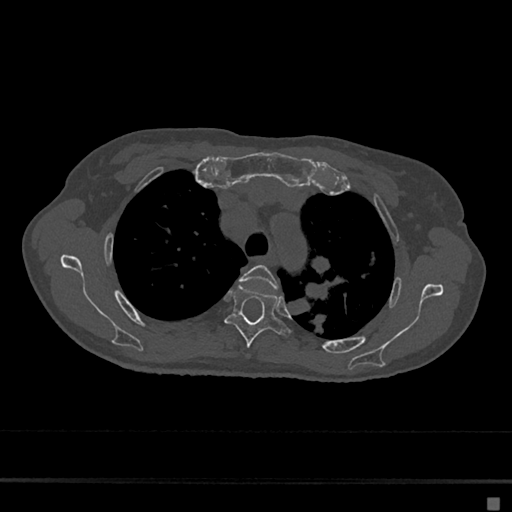
CT including the spine, one axial slice. Position 507 of 797 along the scan axis. Reconstruction kernel Br40s/3. 120 kVp. Bone window (W 1800 / L 400 HU). 512 × 512 image matrix, field of view 360 × 360 mm. Female patient, age 68 years. Case-level facts recorded for this patient, not image findings: primary cancer: renal.
Structures marked on this image (semi-automatically segmented with operator editing):
- T3 vertebra: bounding box (x1, y1, x2, y2) in pixels: (240, 265, 278, 290)
- T4 vertebra: (225, 284, 291, 347)